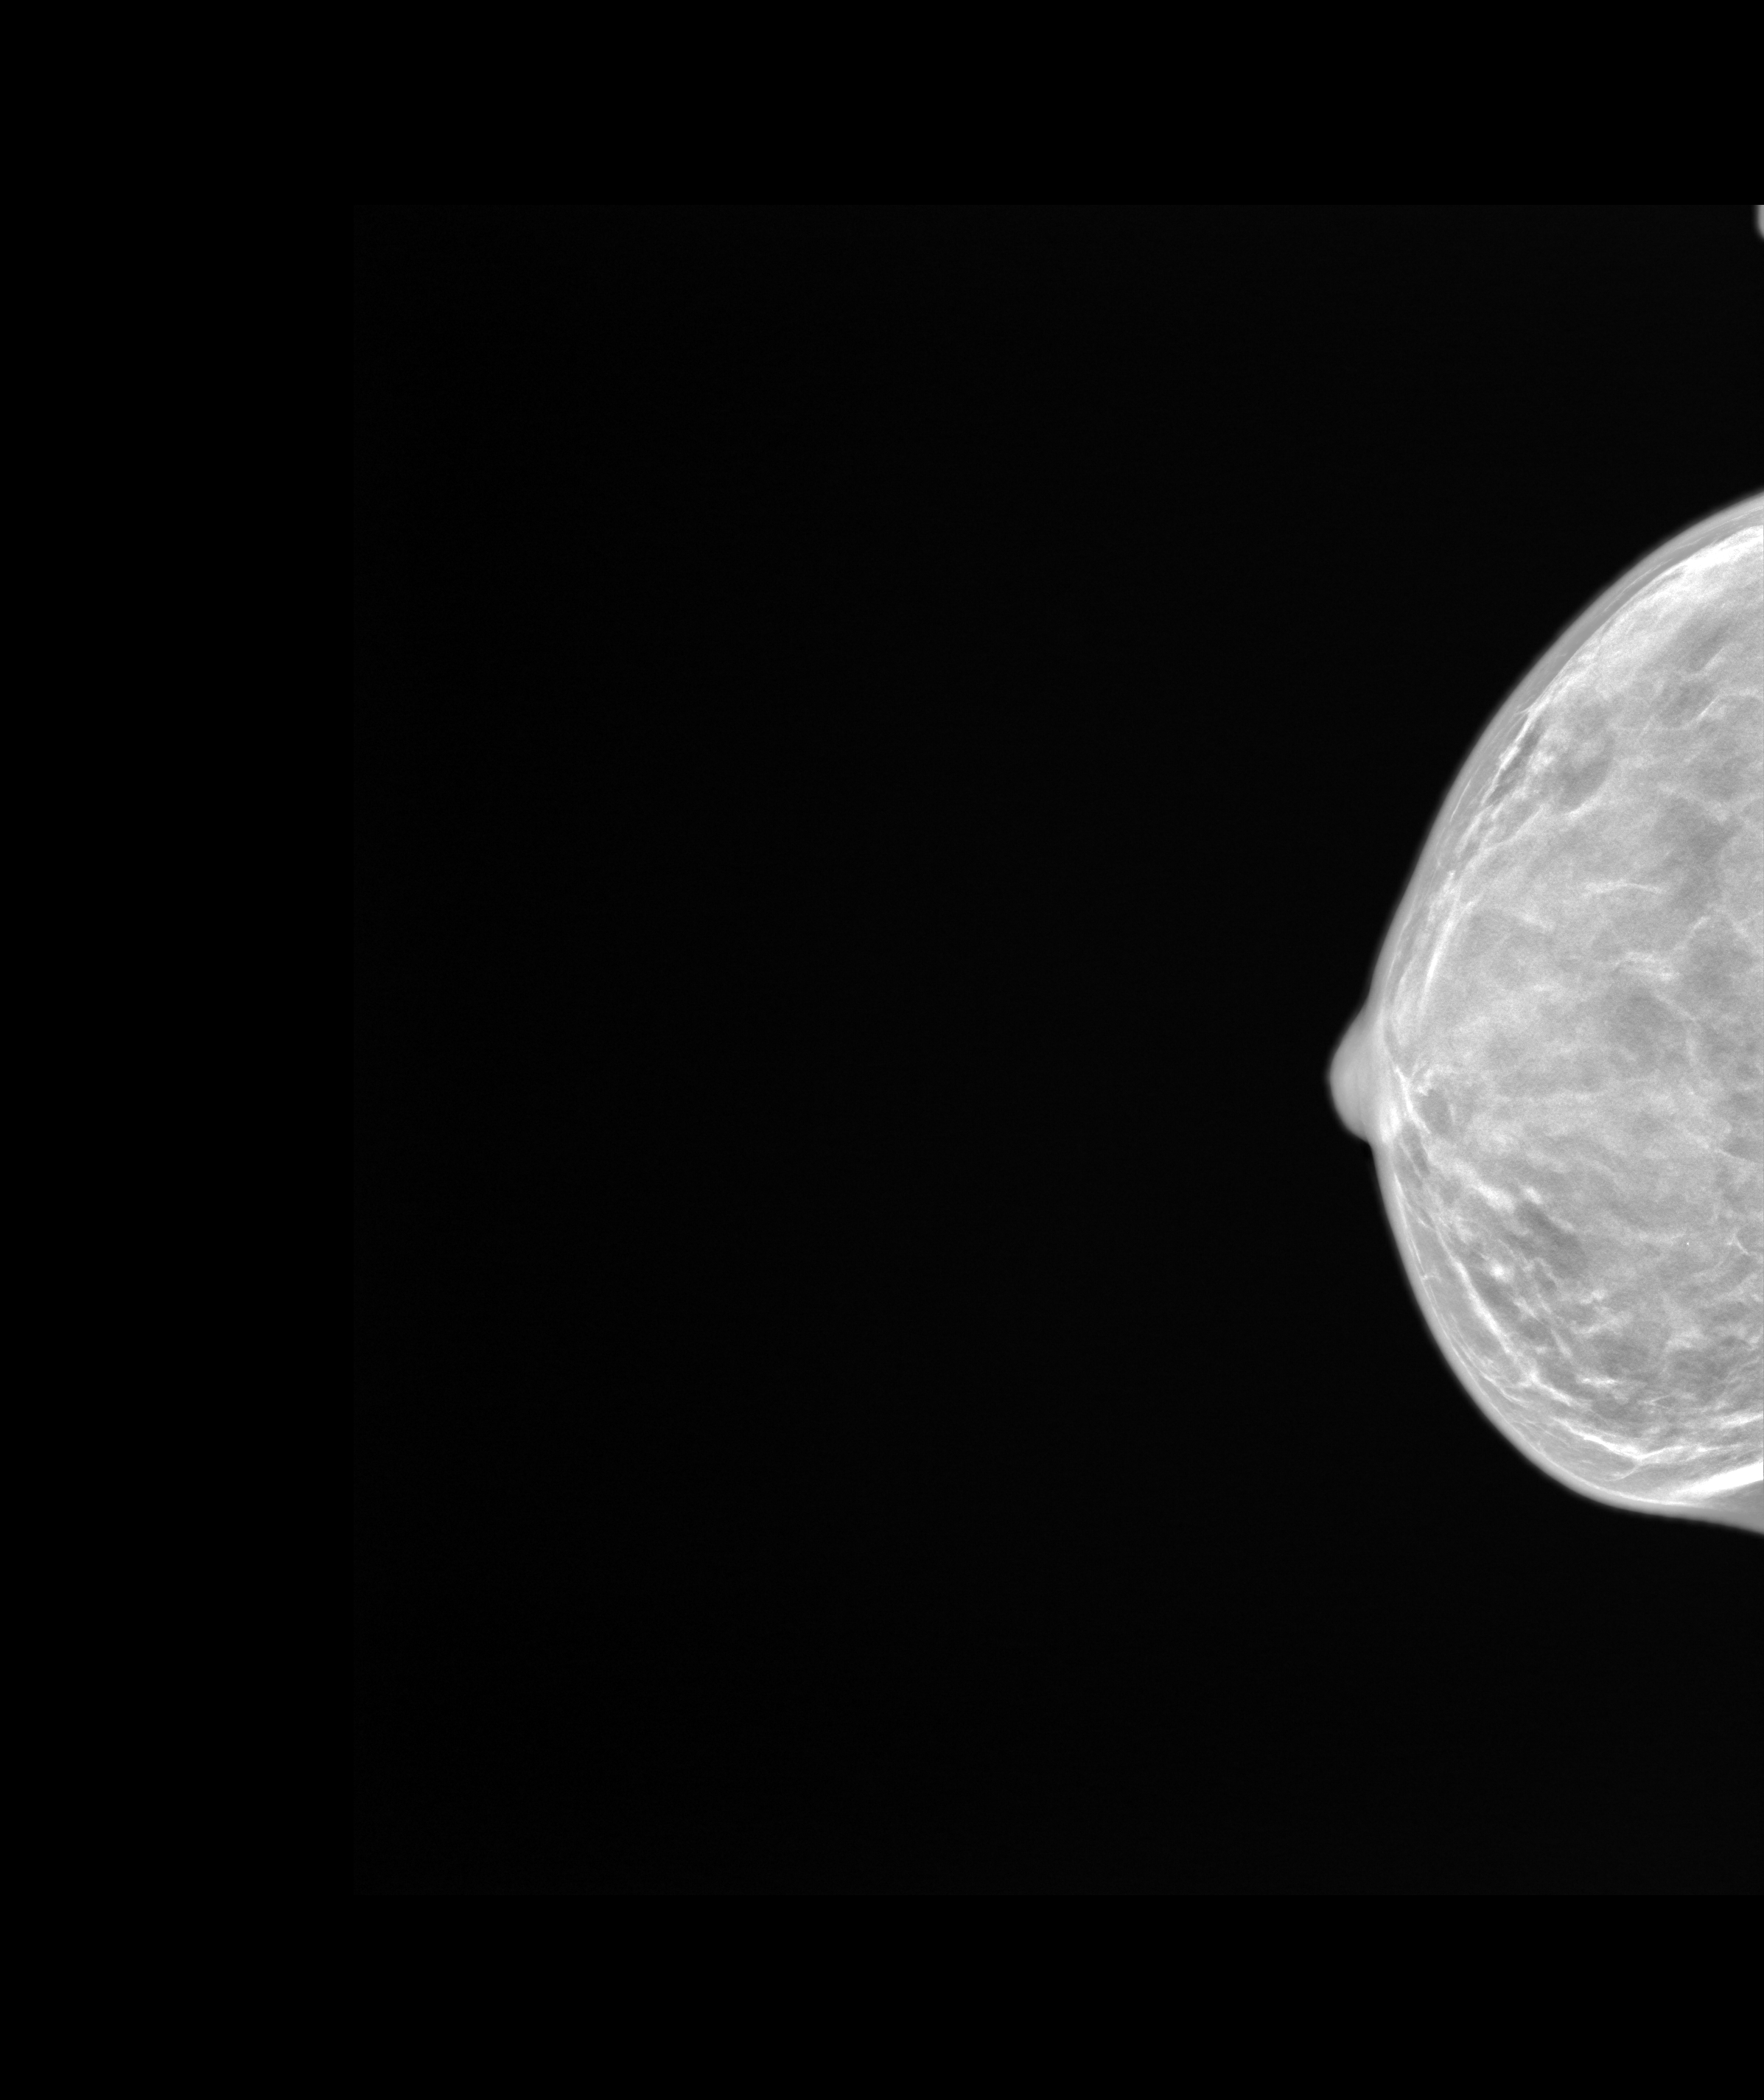
Synthesized 2-D mammogram reconstructed from digital breast tomosynthesis, right breast, craniocaudal (CC) view, annual screening mammography examination, system: SenoIris_1SP1.1(421). Female patient, age 54 years.
BI-RADS breast density category at the screening exam (both breasts, scale 1–4): 4. Final BI-RADS category for the screening round (tomosynthesis exam, both breasts): category 1. Recall: no recall after this screen.